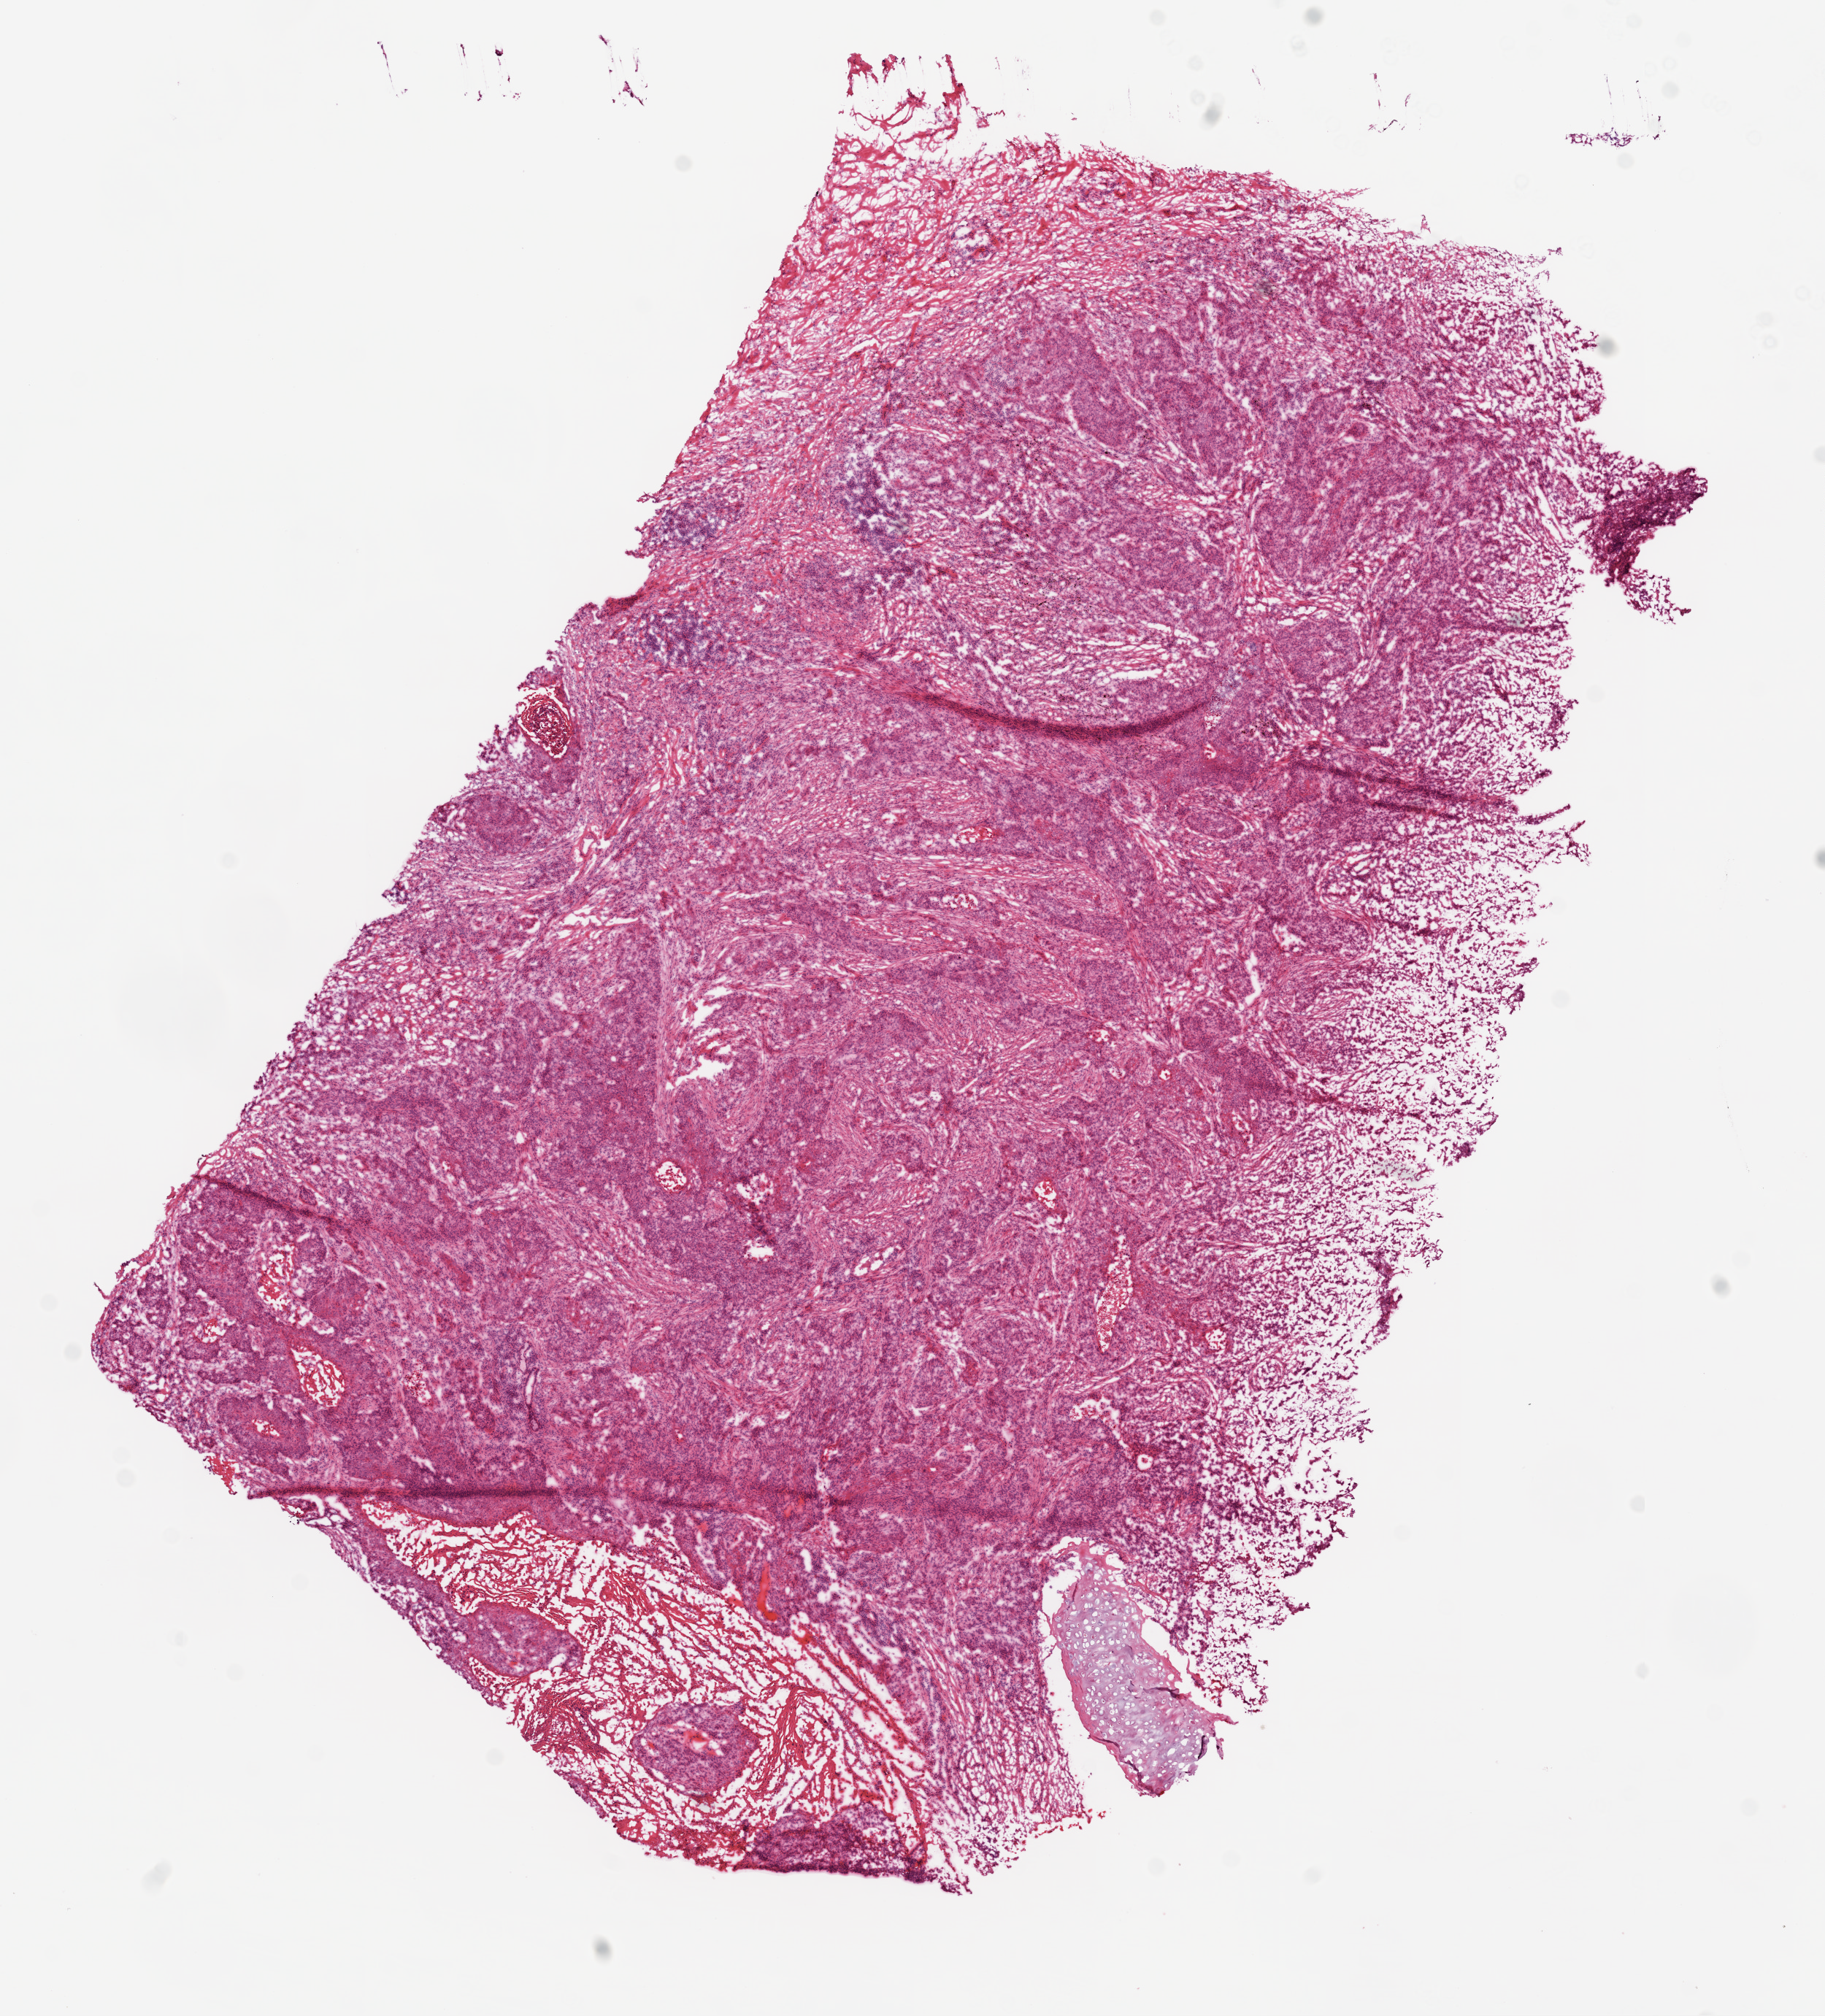
Digitized H&E-stained tissue section (whole slide) — low-resolution overview of the scanned area, about 10.0 x 11.1 mm (from a 20x scan), frozen section from the top of the tissue portion, primary tumour sample from the lung. Patient: male, age at initial diagnosis 75 years. Slide review estimates, as recorded: tumour cells 75%, tumour nuclei 65%, normal cells 0%, stromal cells 20%, necrosis 5%. Infiltration values recorded for this section: lymphocyte infiltration 20%, monocyte infiltration 1%, neutrophil infiltration 5%.
Laterality: left. Diagnosis: Squamous cell carcinoma, NOS (lower lobe, lung). AJCC pathologic stage: IB. TNM: T2 N0 M0.